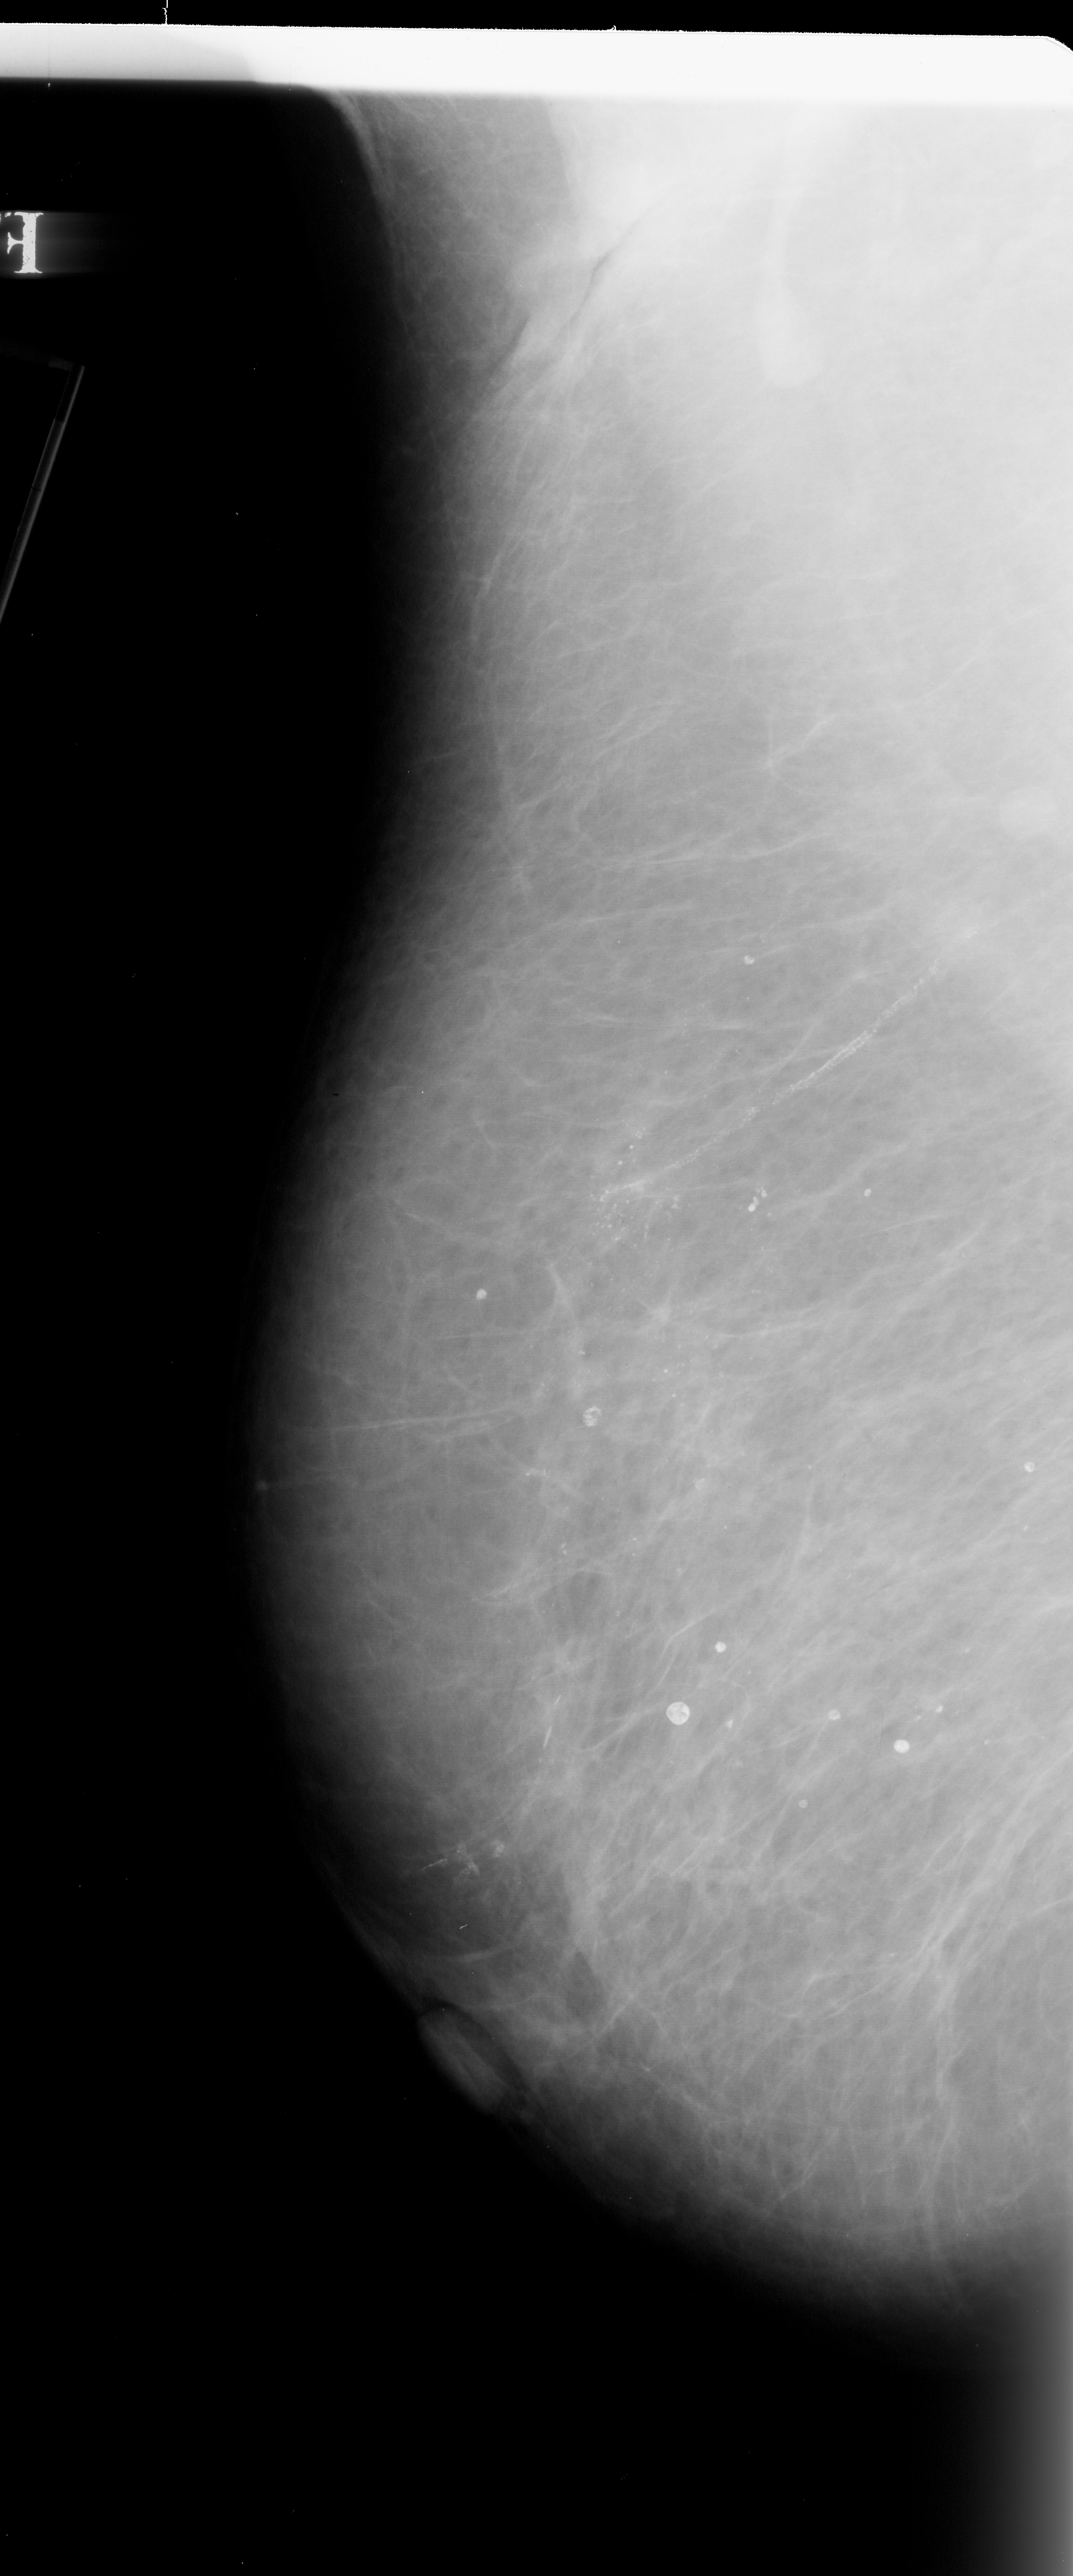
Scanned film-screen mammogram, left breast, MLO view, breast composition: scattered fibroglandular densities (BI-RADS density category 2 of 4).
Calcifications, morphology pleomorphic, distribution segmental; BI-RADS assessment category 4; subtlety rating 3 on a 1 (subtle) to 5 (obvious) scale; pathology (as recorded): malignant.